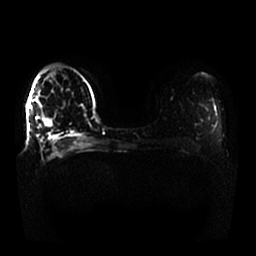
Breast MRI, one axial slice; diffusion-weighted series; image 2 of 4 stored at this slice position (different b-values; order by instance number); 1.5 T; 256 × 256 image matrix. Female patient.
Annotated regions visible in this slice (outlined manually by an expert reader):
- tumour on diffusion-weighted imaging: bounding box [x1, y1, x2, y2] px = [44, 118, 53, 128]